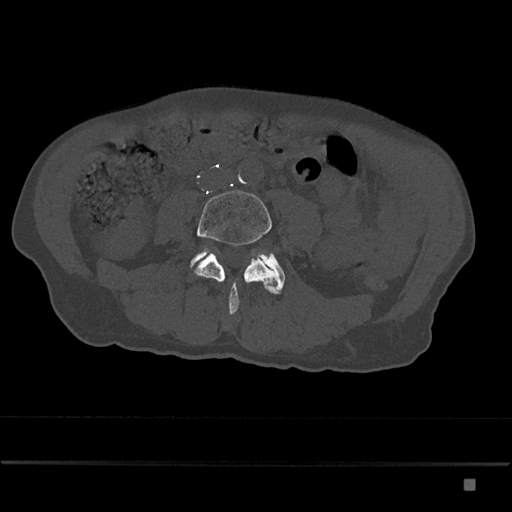
CT including the spine, one axial slice; slice 325 of 797 in the series (ordered by position); reconstruction kernel Br40s/3; 120 kVp; bone window (W 1800 / L 400 HU); 0.5 mm slice thickness; 512 × 512 image matrix. Patient: male, 72 years. Case-level facts recorded for this patient, not image findings: primary cancer: prostate.
Annotated regions visible in this slice (semi-automatically segmented with operator editing):
- L4 vertebra: bounding box <191,190,280,315> (left, top, right, bottom; pixels)
- L5 vertebra: <191,248,285,294>